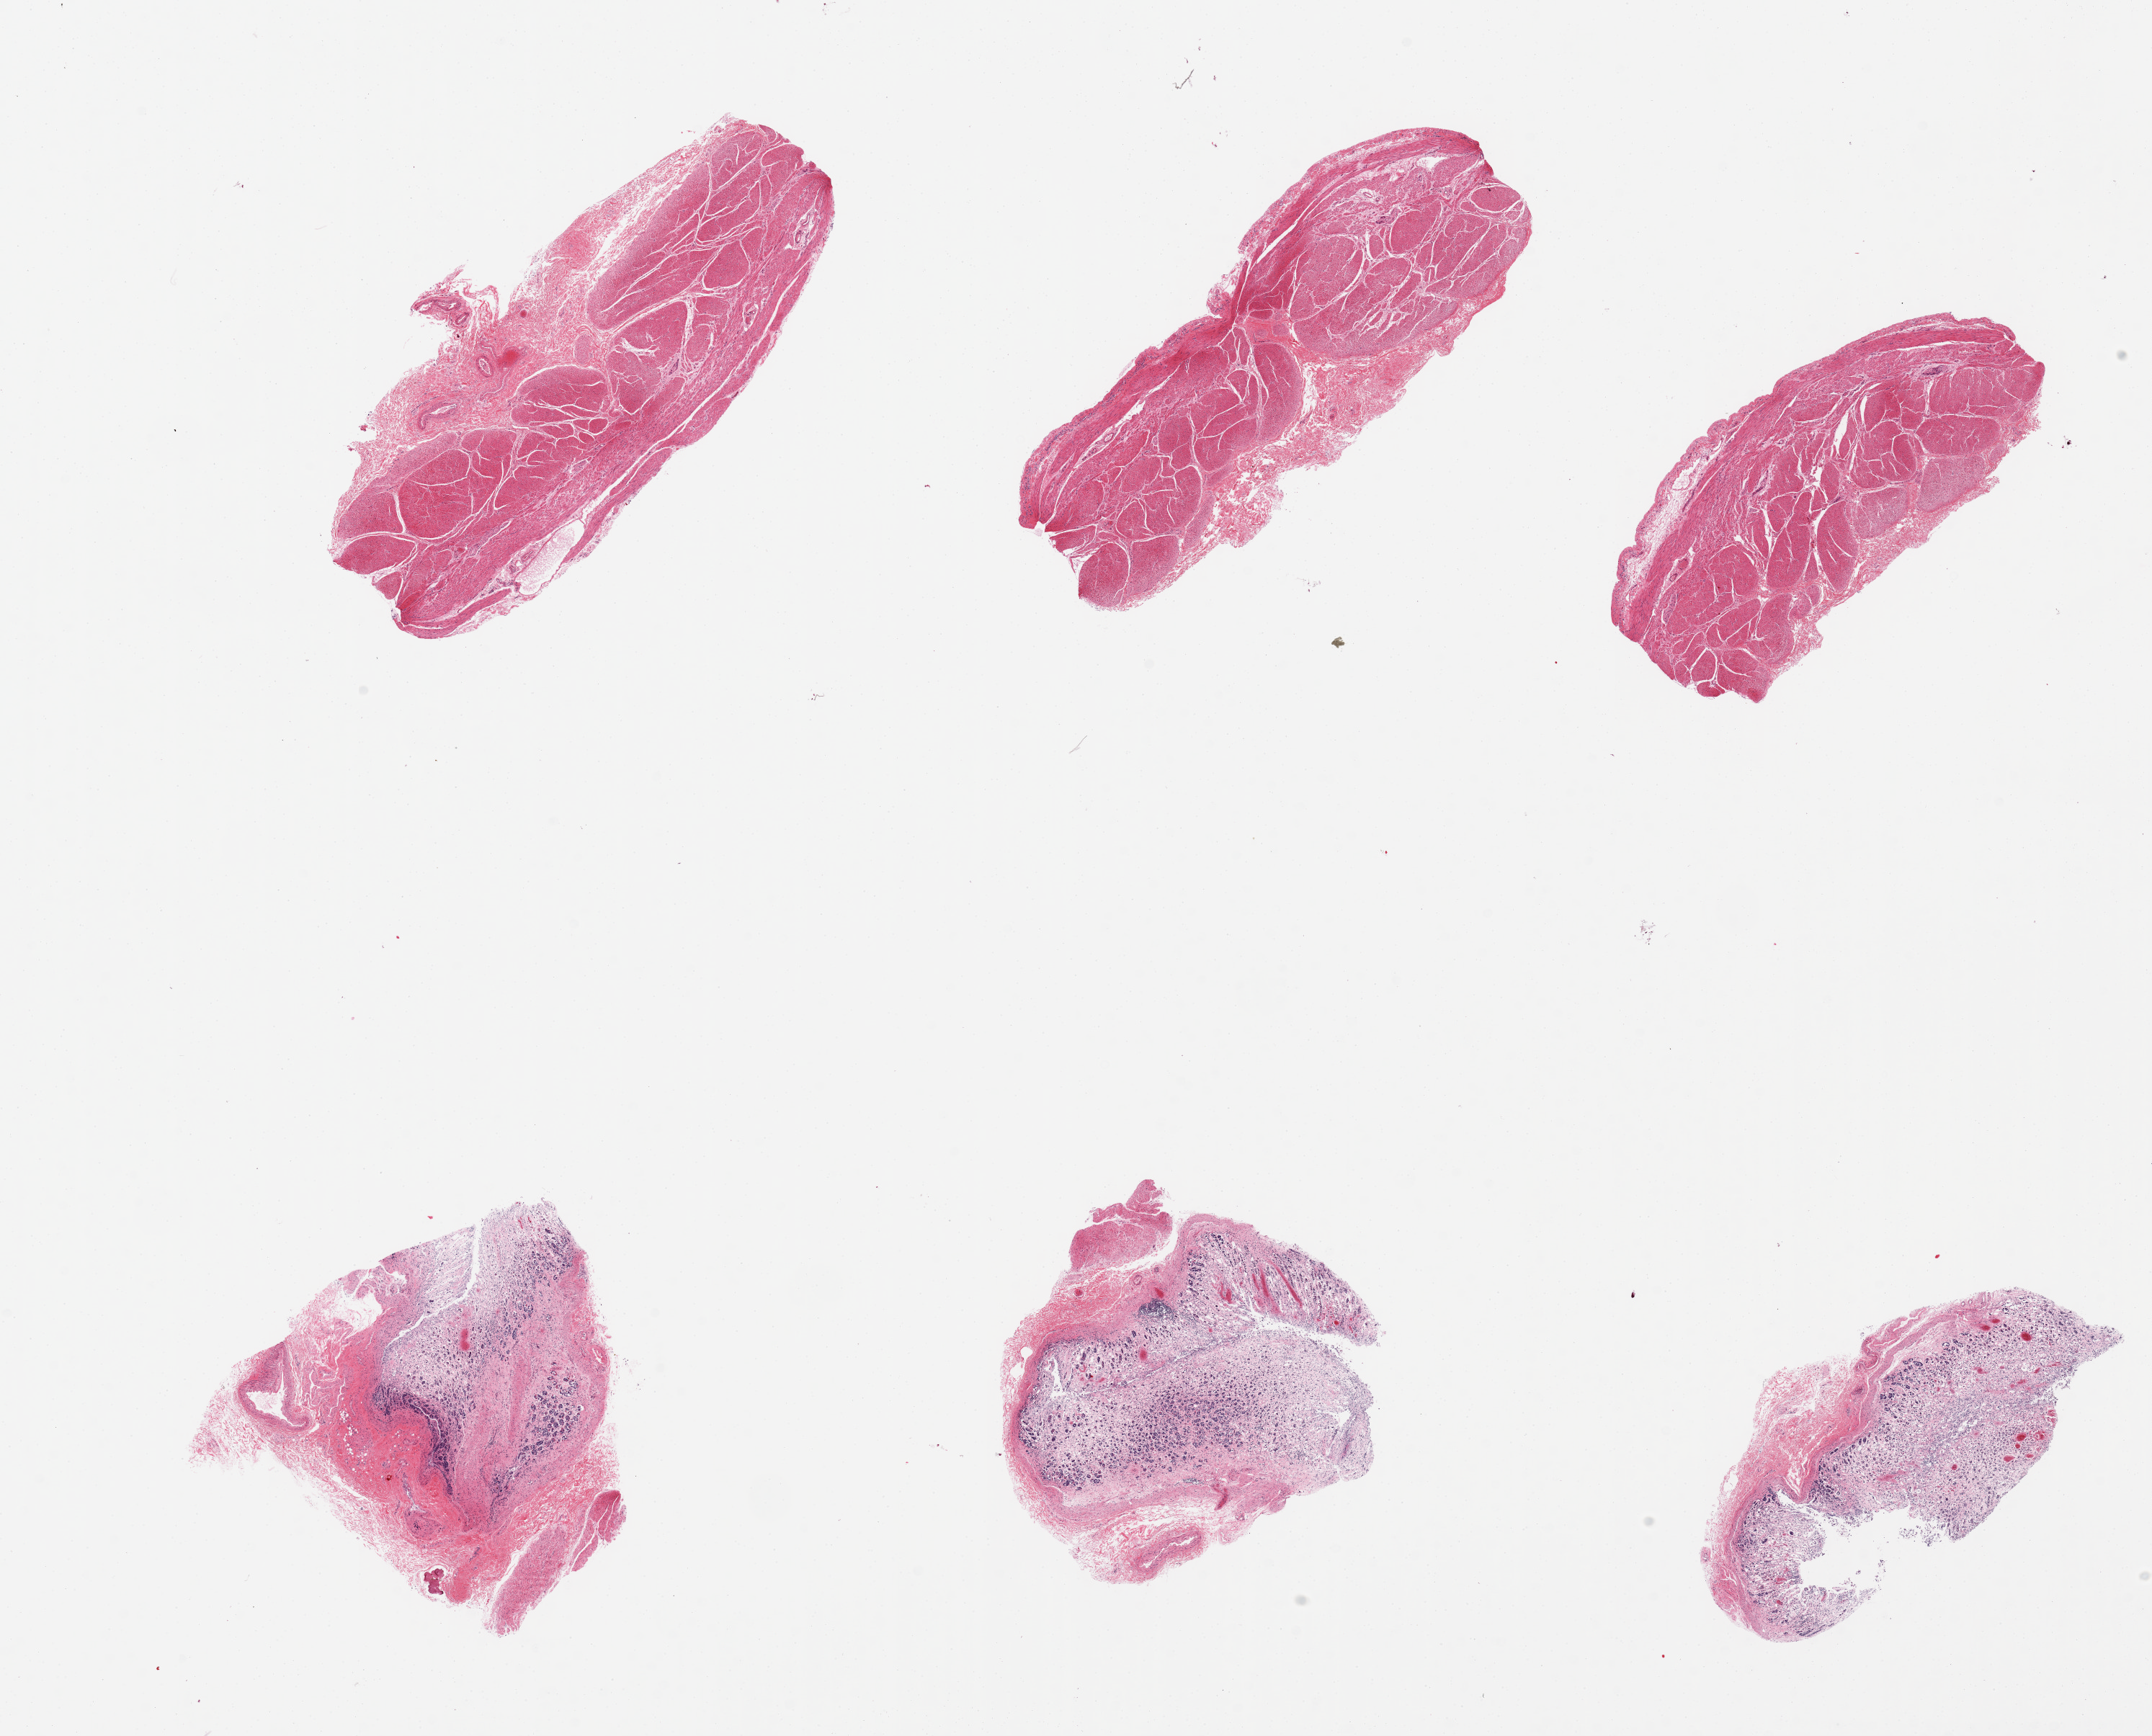
Digitized H&E-stained section, brightfield, whole scanned area (about 23.6 x 19.1 mm, from a 20x scan) shown as a low-resolution overview; PAXgene-fixed, paraffin-embedded tissue; section of stomach (target tissue); tissue donor sample. Female donor.
Pathologist's review note for this sample: 6 pieces; mucosa either completely sloughed; or completely autolyzed.